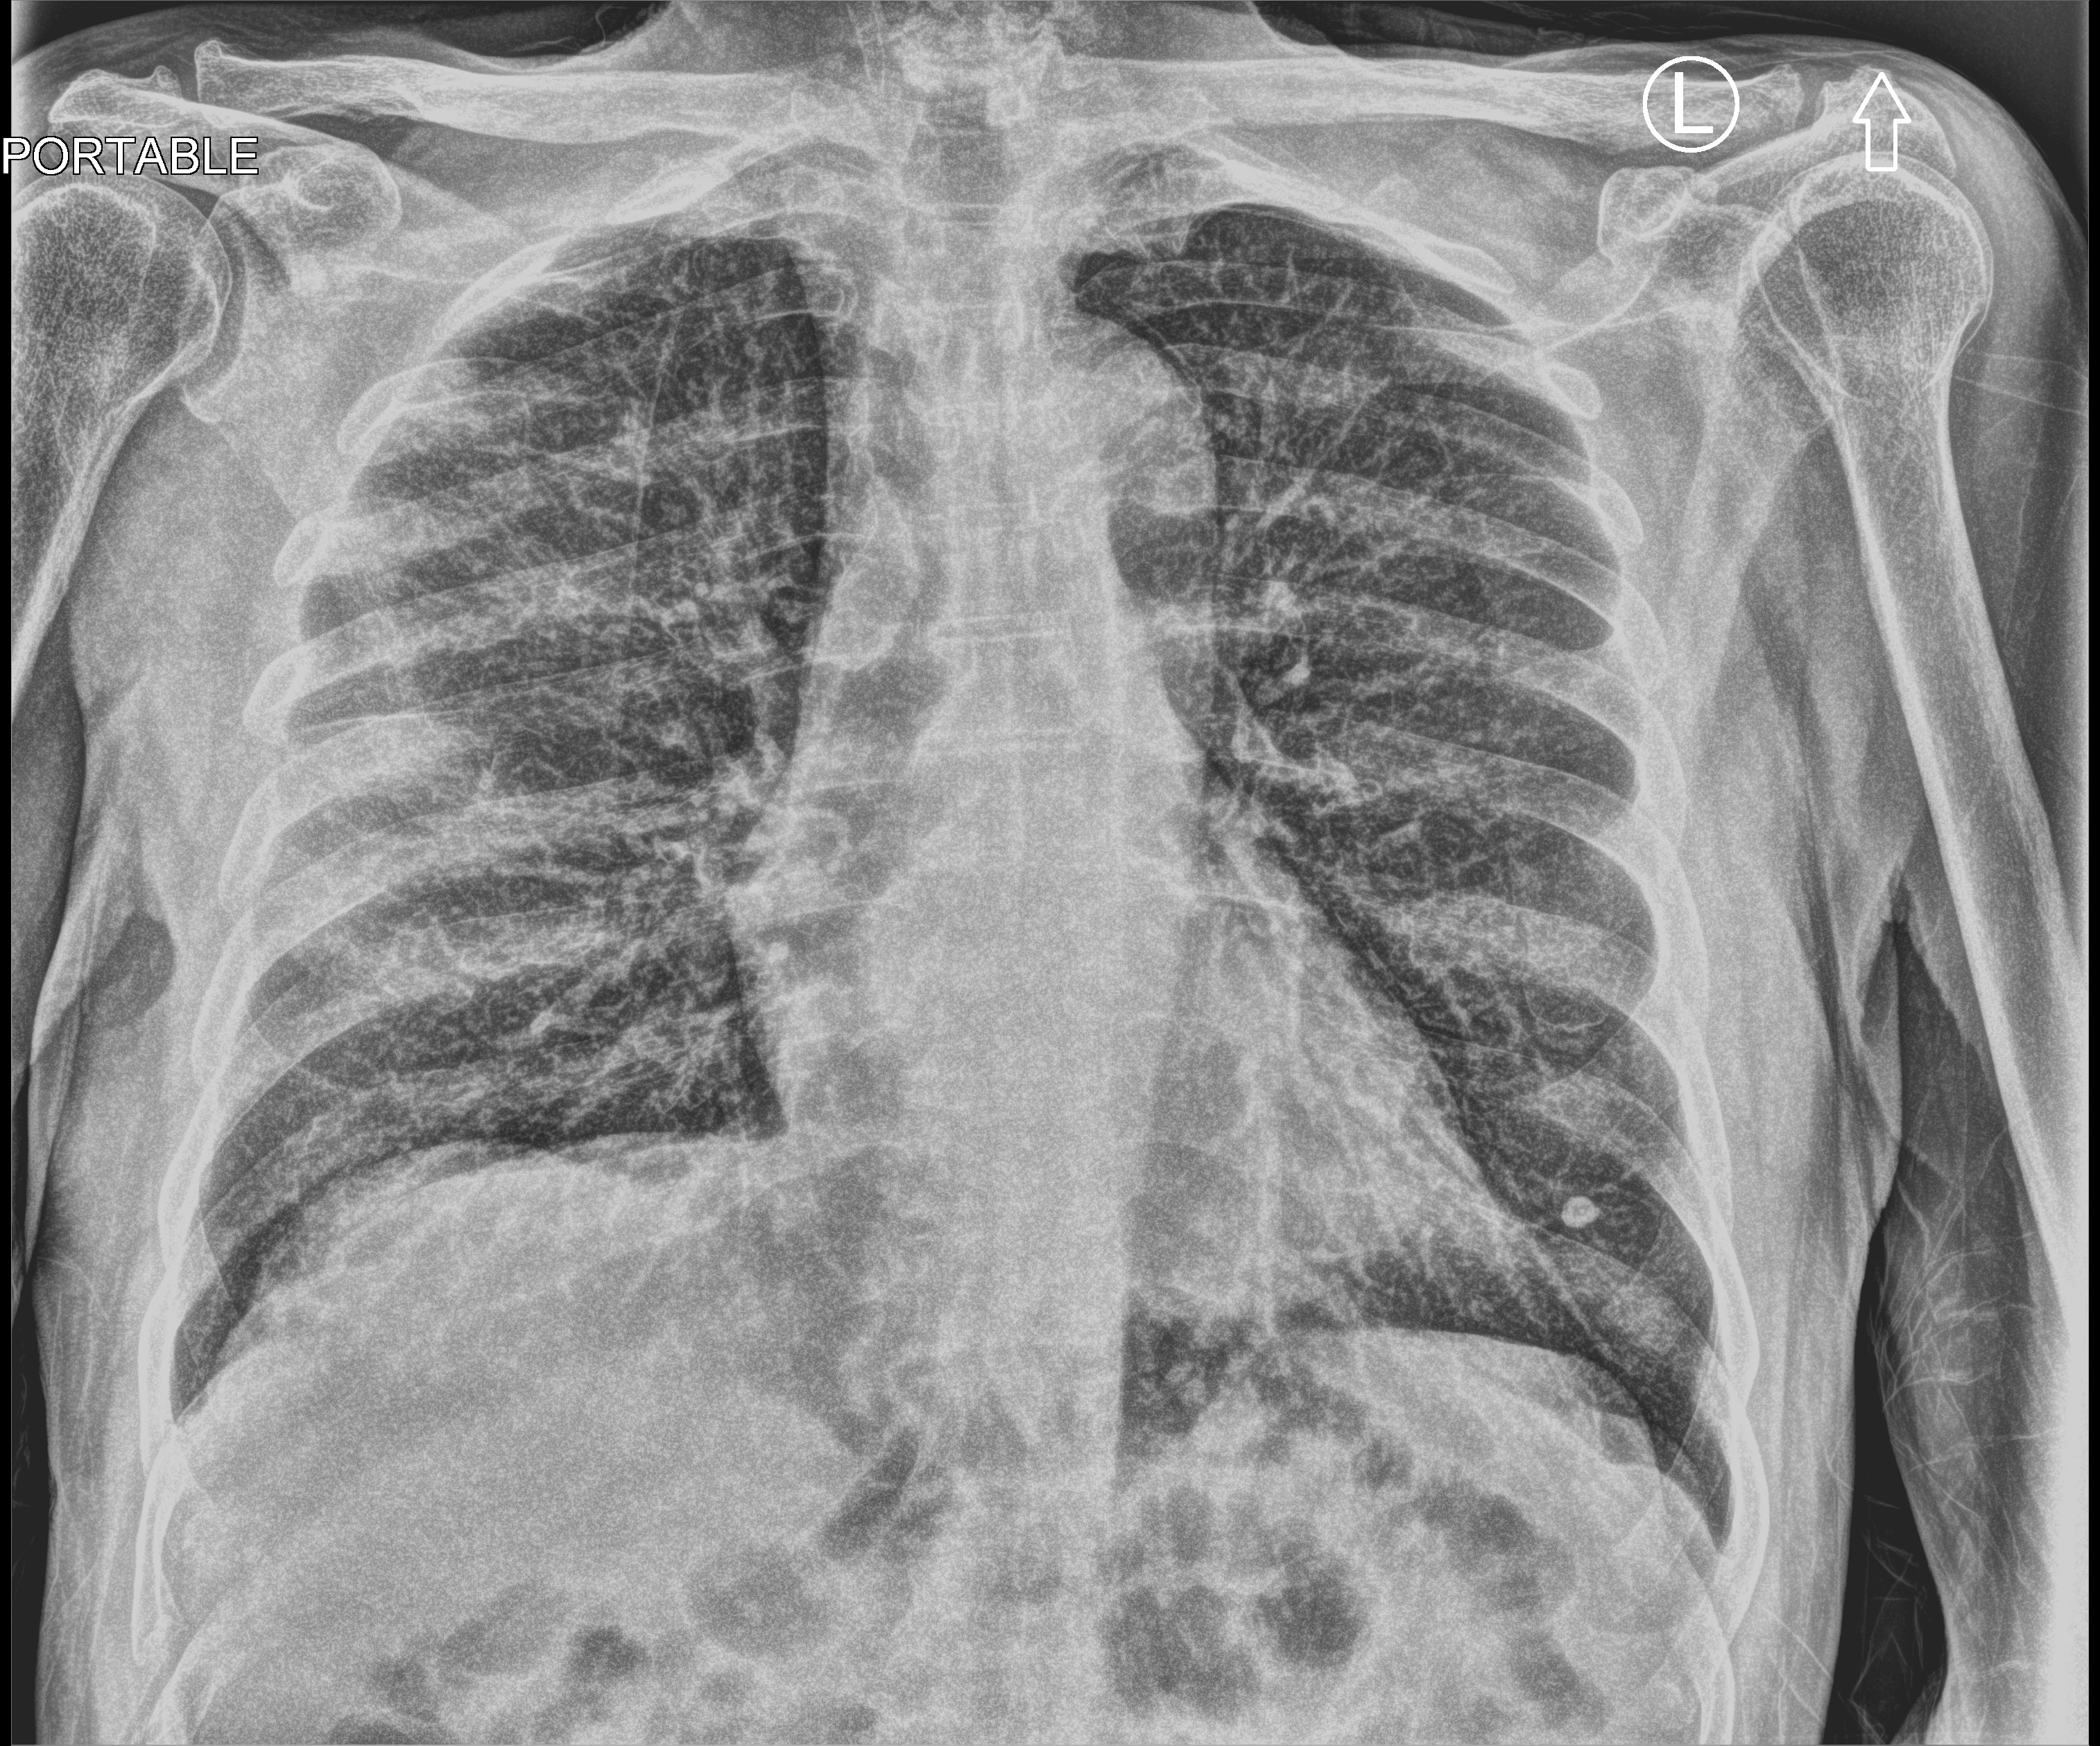
Portable chest radiograph; anteroposterior (AP) projection. Patient hospitalised with COVID-19; male, aged 75–90 years.
From the hospital-stay record, not from the radiograph (when in the stay this image was taken is not recorded):
- mechanically ventilated during this hospital stay: no
- smoking status (admission record): former